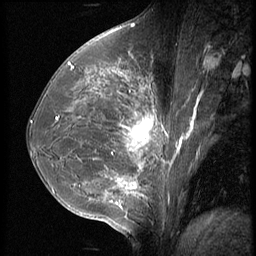
Breast MRI (dynamic contrast-enhanced), one sagittal slice. Position 28 of 56 along the scan axis. 3 images stored at this slice position (order not interpretable as contrast timing). 1.5 T. TE 4.2 ms, TR 9 ms. 2.5 mm slice thickness. 256 × 256 image matrix, field of view 180 × 180 mm. Patient: female, 35 years. From the clinical record (not read from this slice): setting: breast cancer imaged before/during neoadjuvant chemotherapy; receptor status: HR-positive, HER2-negative.
Annotated regions visible in this slice (semi-automatic segmentation, software-assisted and operator-edited):
- analysis volume of interest (the breast-tissue region the enhancement analysis was run in; not a lesion): bounding box (x1, y1, x2, y2) in pixels: (63, 60, 188, 218)
- tumour enhancement mask (voxels above the 140 % enhancement threshold inside the analysis volume of interest): (69, 64, 169, 203)